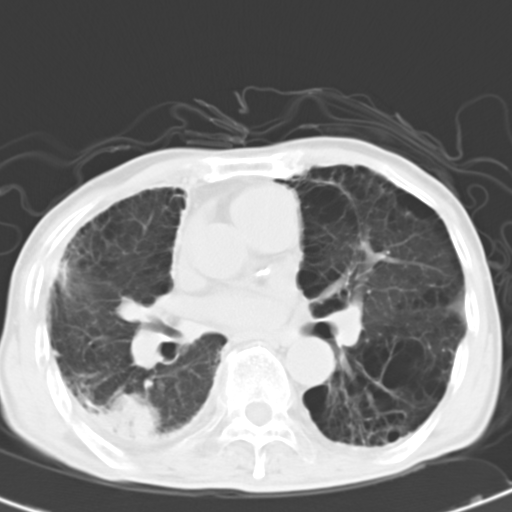
Chest CT, one axial slice. Slice 15 of 31 in the series (ordered by position). 120 kVp. Lung window (W 1500 / L -600 HU). 512 × 512 image matrix, field of view 279 × 279 mm. Male patient, age 67 years. Case-level facts recorded for this patient, not image findings: clinical TNM (as recorded): T2 N3 M1.
Annotated regions visible in this slice (rectangle marked by the reading radiologist):
- lung tumour (recorded histology: adenocarcinoma): bounding box [x1, y1, x2, y2] px = [90, 381, 163, 456]